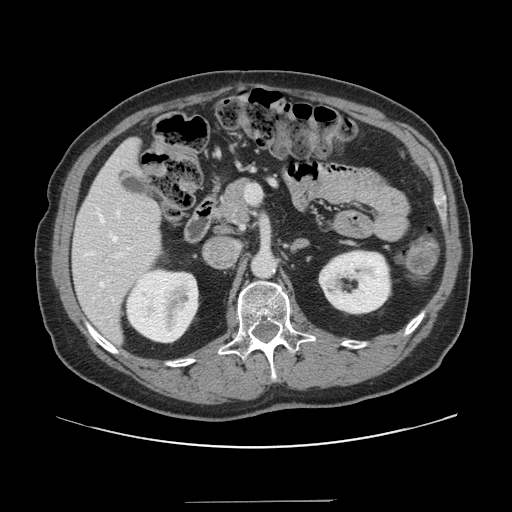
Contrast-enhanced abdominal CT, one axial slice. Position 73 of 151 along the scan axis. Intravenous contrast given. Soft-tissue window (W 400 / L 40 HU). 2.5 mm slice thickness. 512 × 512 image matrix, field of view 399 × 399 mm. Male patient, age 63 years. Case-level facts recorded for this patient, not image findings: diagnosis: colorectal cancer liver metastases, imaged before liver resection; multiple liver metastases: no; largest metastasis: 2.1 cm.
Outlined on this slice (expert manual segmentation):
- hepatic veins: bounding box [x1, y1, x2, y2] px = [97, 211, 120, 287]
- liver: [73, 139, 162, 343]
- planned liver remnant (the part of the liver to remain after resection): [73, 140, 162, 343]
- portal vein (with intrahepatic branches): [113, 185, 261, 258]